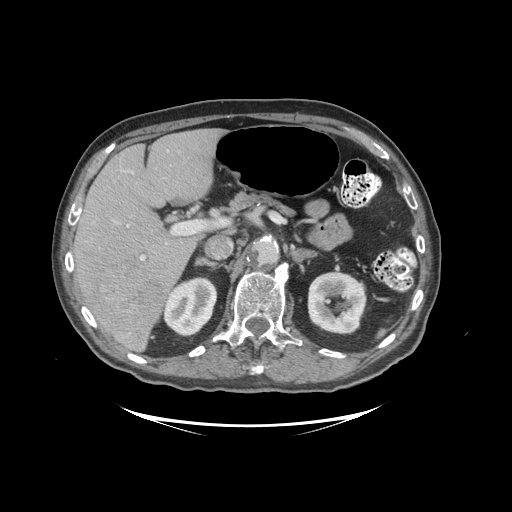
Contrast-enhanced abdominal CT (liver protocol), one axial slice. Slice 58 of 99 in the series (ordered by position). Reconstruction kernel STANDARD. 140 kVp. Soft-tissue window (W 400 / L 40 HU). 512 × 512 image matrix, field of view 460 × 460 mm. From the clinical record (not read from this slice): diagnosis: hepatocellular carcinoma (patient treated with transarterial chemoembolisation; whether this scan precedes or follows treatment is not stated here); TNM stage (as recorded): Stage-I; Child-Pugh class: A.
Outlined on this slice (semi-automatic segmentation, software-assisted and operator-edited):
- liver parenchyma outside the tumour (the mass and vessels are separate outlines, so this box may not span the whole liver): box from (x=72, y=128) to (x=222, y=350) px
- mass: (x=76, y=250)–(x=164, y=346)
- liver vessels: (x=140, y=226)–(x=201, y=261)